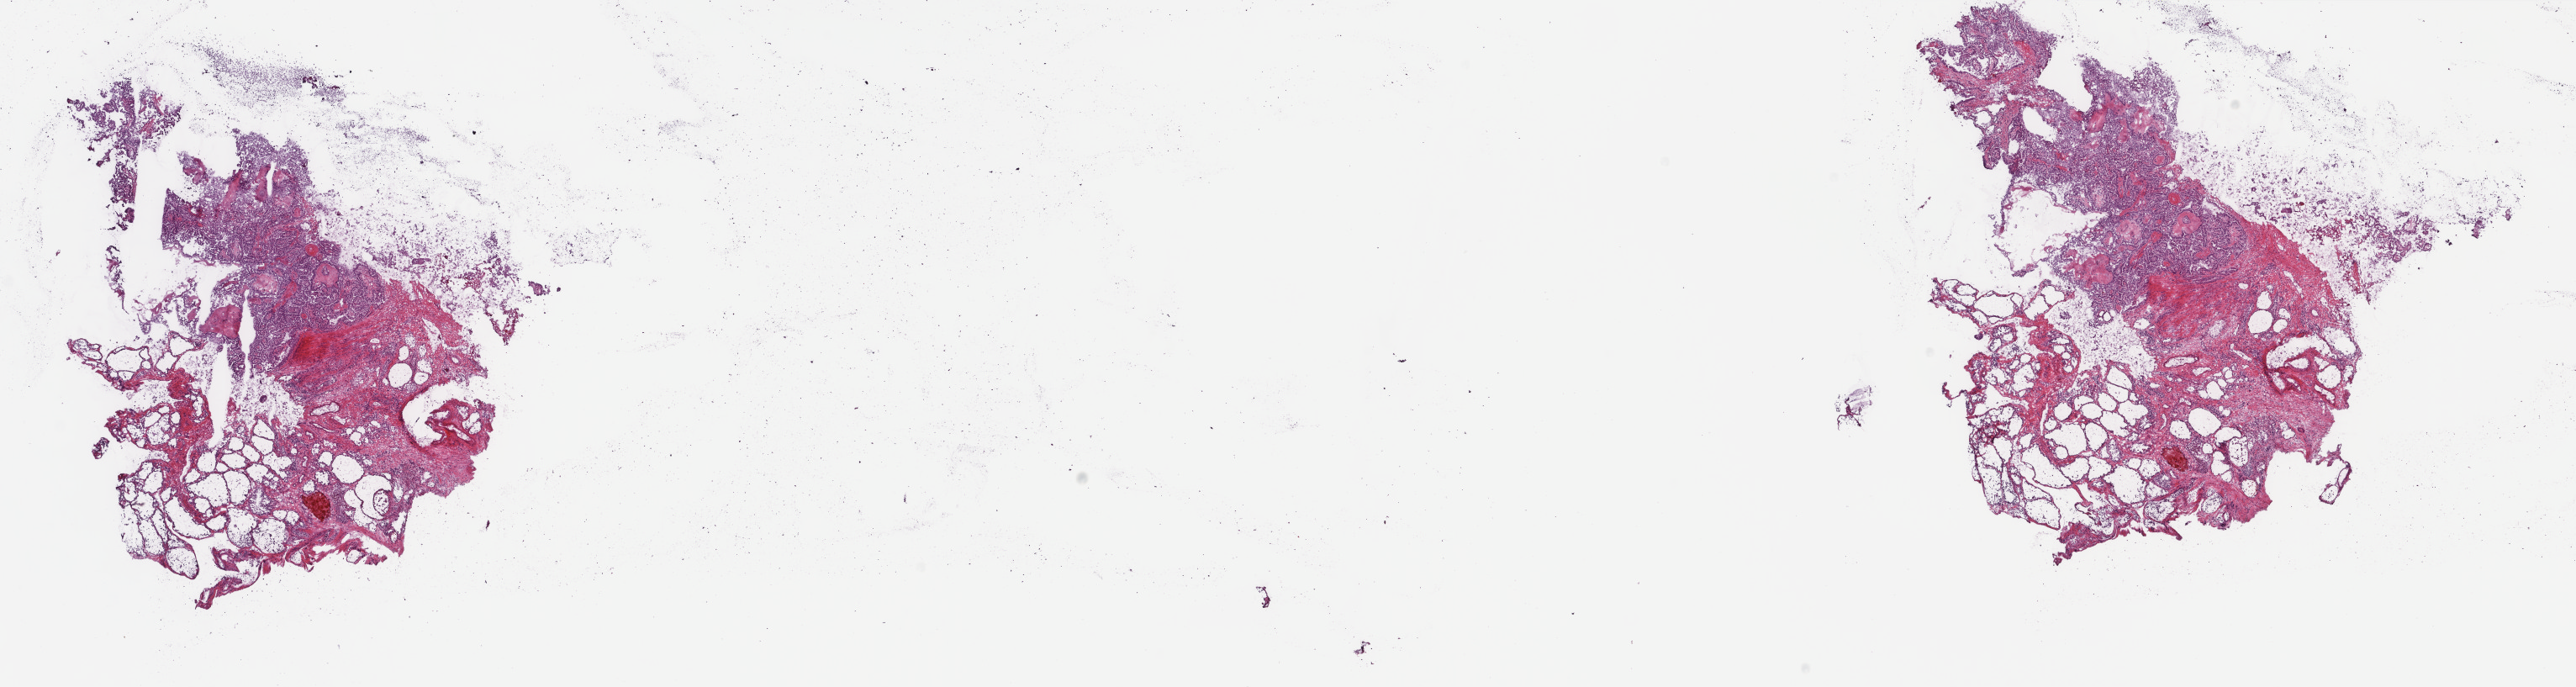
H&E whole-slide image, shown as a low-resolution overview of the whole scanned area (about 24.3 x 6.5 mm). Frozen section from the top of the tissue portion. Primary tumour sample from the thyroid. Female, age 28 years at initial diagnosis. Composition of this section per pathologist review: tumour cells 50%, tumour nuclei 100%, normal cells 0%, stromal cells 50%, necrosis 0%. Infiltration values recorded for this section: lymphocyte infiltration 1%, monocyte infiltration 1%, neutrophil infiltration 0%.
Diagnosis: Papillary carcinoma, columnar cell (thyroid gland). Lymph nodes positive (case pathology): 8 of 16 examined. AJCC pathologic stage: I.